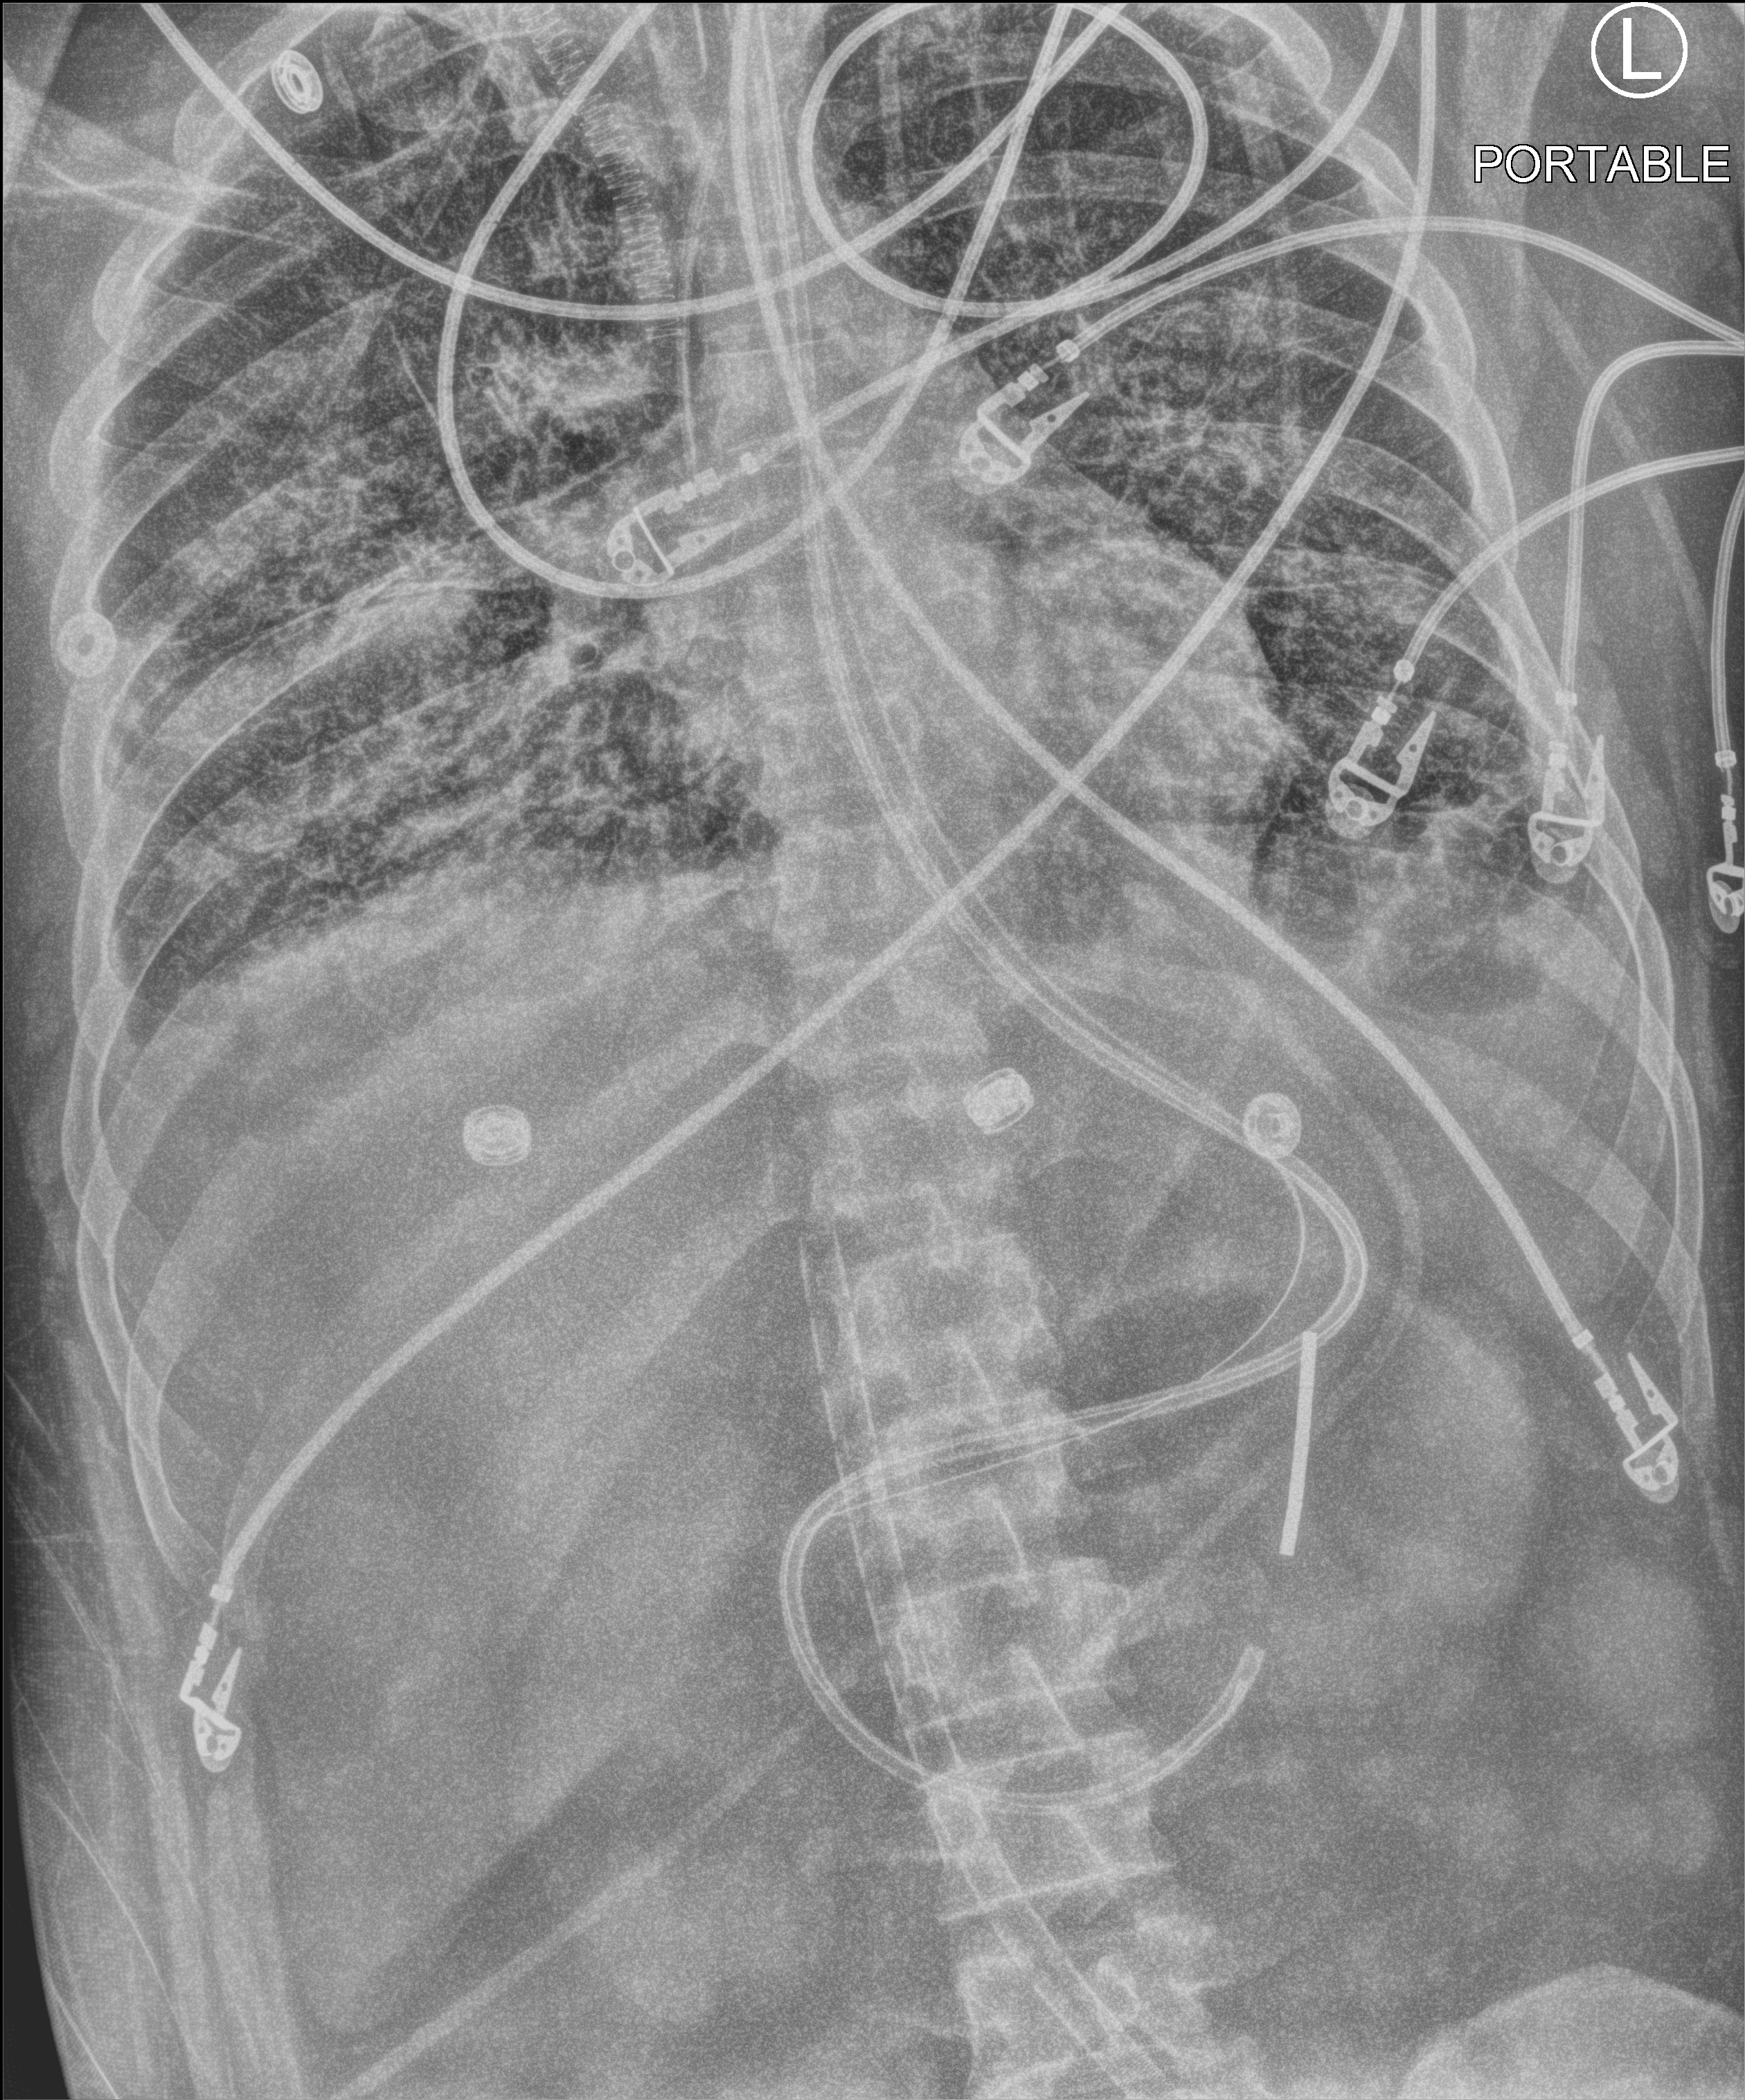
Portable chest radiograph; anteroposterior (AP) projection. Adult patient hospitalised with COVID-19, age 18–59 years.
From the hospital-stay record, not from the radiograph (when in the stay this image was taken is not recorded): admitted to intensive care during this hospital stay: yes; other chronic lung disease (admission record): no; mechanically ventilated during this hospital stay: yes.